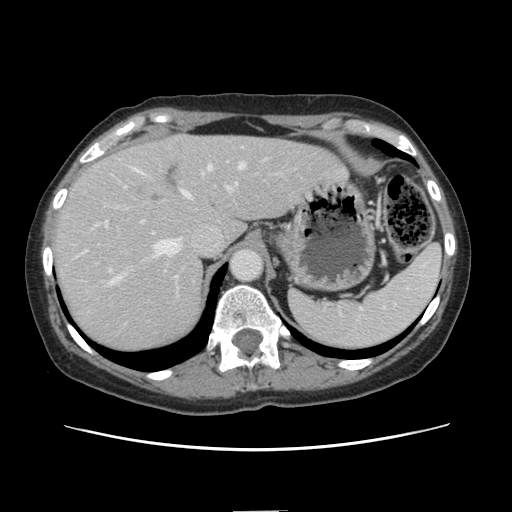
Contrast-enhanced abdominal CT, one axial slice; slice 107 of 141 in the series (ordered by position); 120 kVp; intravenous contrast given; soft-tissue window (W 400 / L 40 HU); 2.5 mm slice thickness; 512 × 512 image matrix, field of view 350 × 350 mm. Female patient, age 63 years. Case-level facts recorded for this patient, not image findings: diagnosis: colorectal cancer liver metastases, imaged before liver resection; multiple liver metastases: yes; largest metastasis: 3.2 cm; chemotherapy before resection: yes.
Structures marked on this image (outlined manually by an expert reader):
- hepatic veins: bounding box [x1, y1, x2, y2] px = [107, 163, 244, 286]
- liver: [53, 135, 344, 352]
- planned liver remnant (the part of the liver to remain after resection): [187, 136, 345, 241]
- portal vein (with intrahepatic branches): [105, 173, 237, 226]